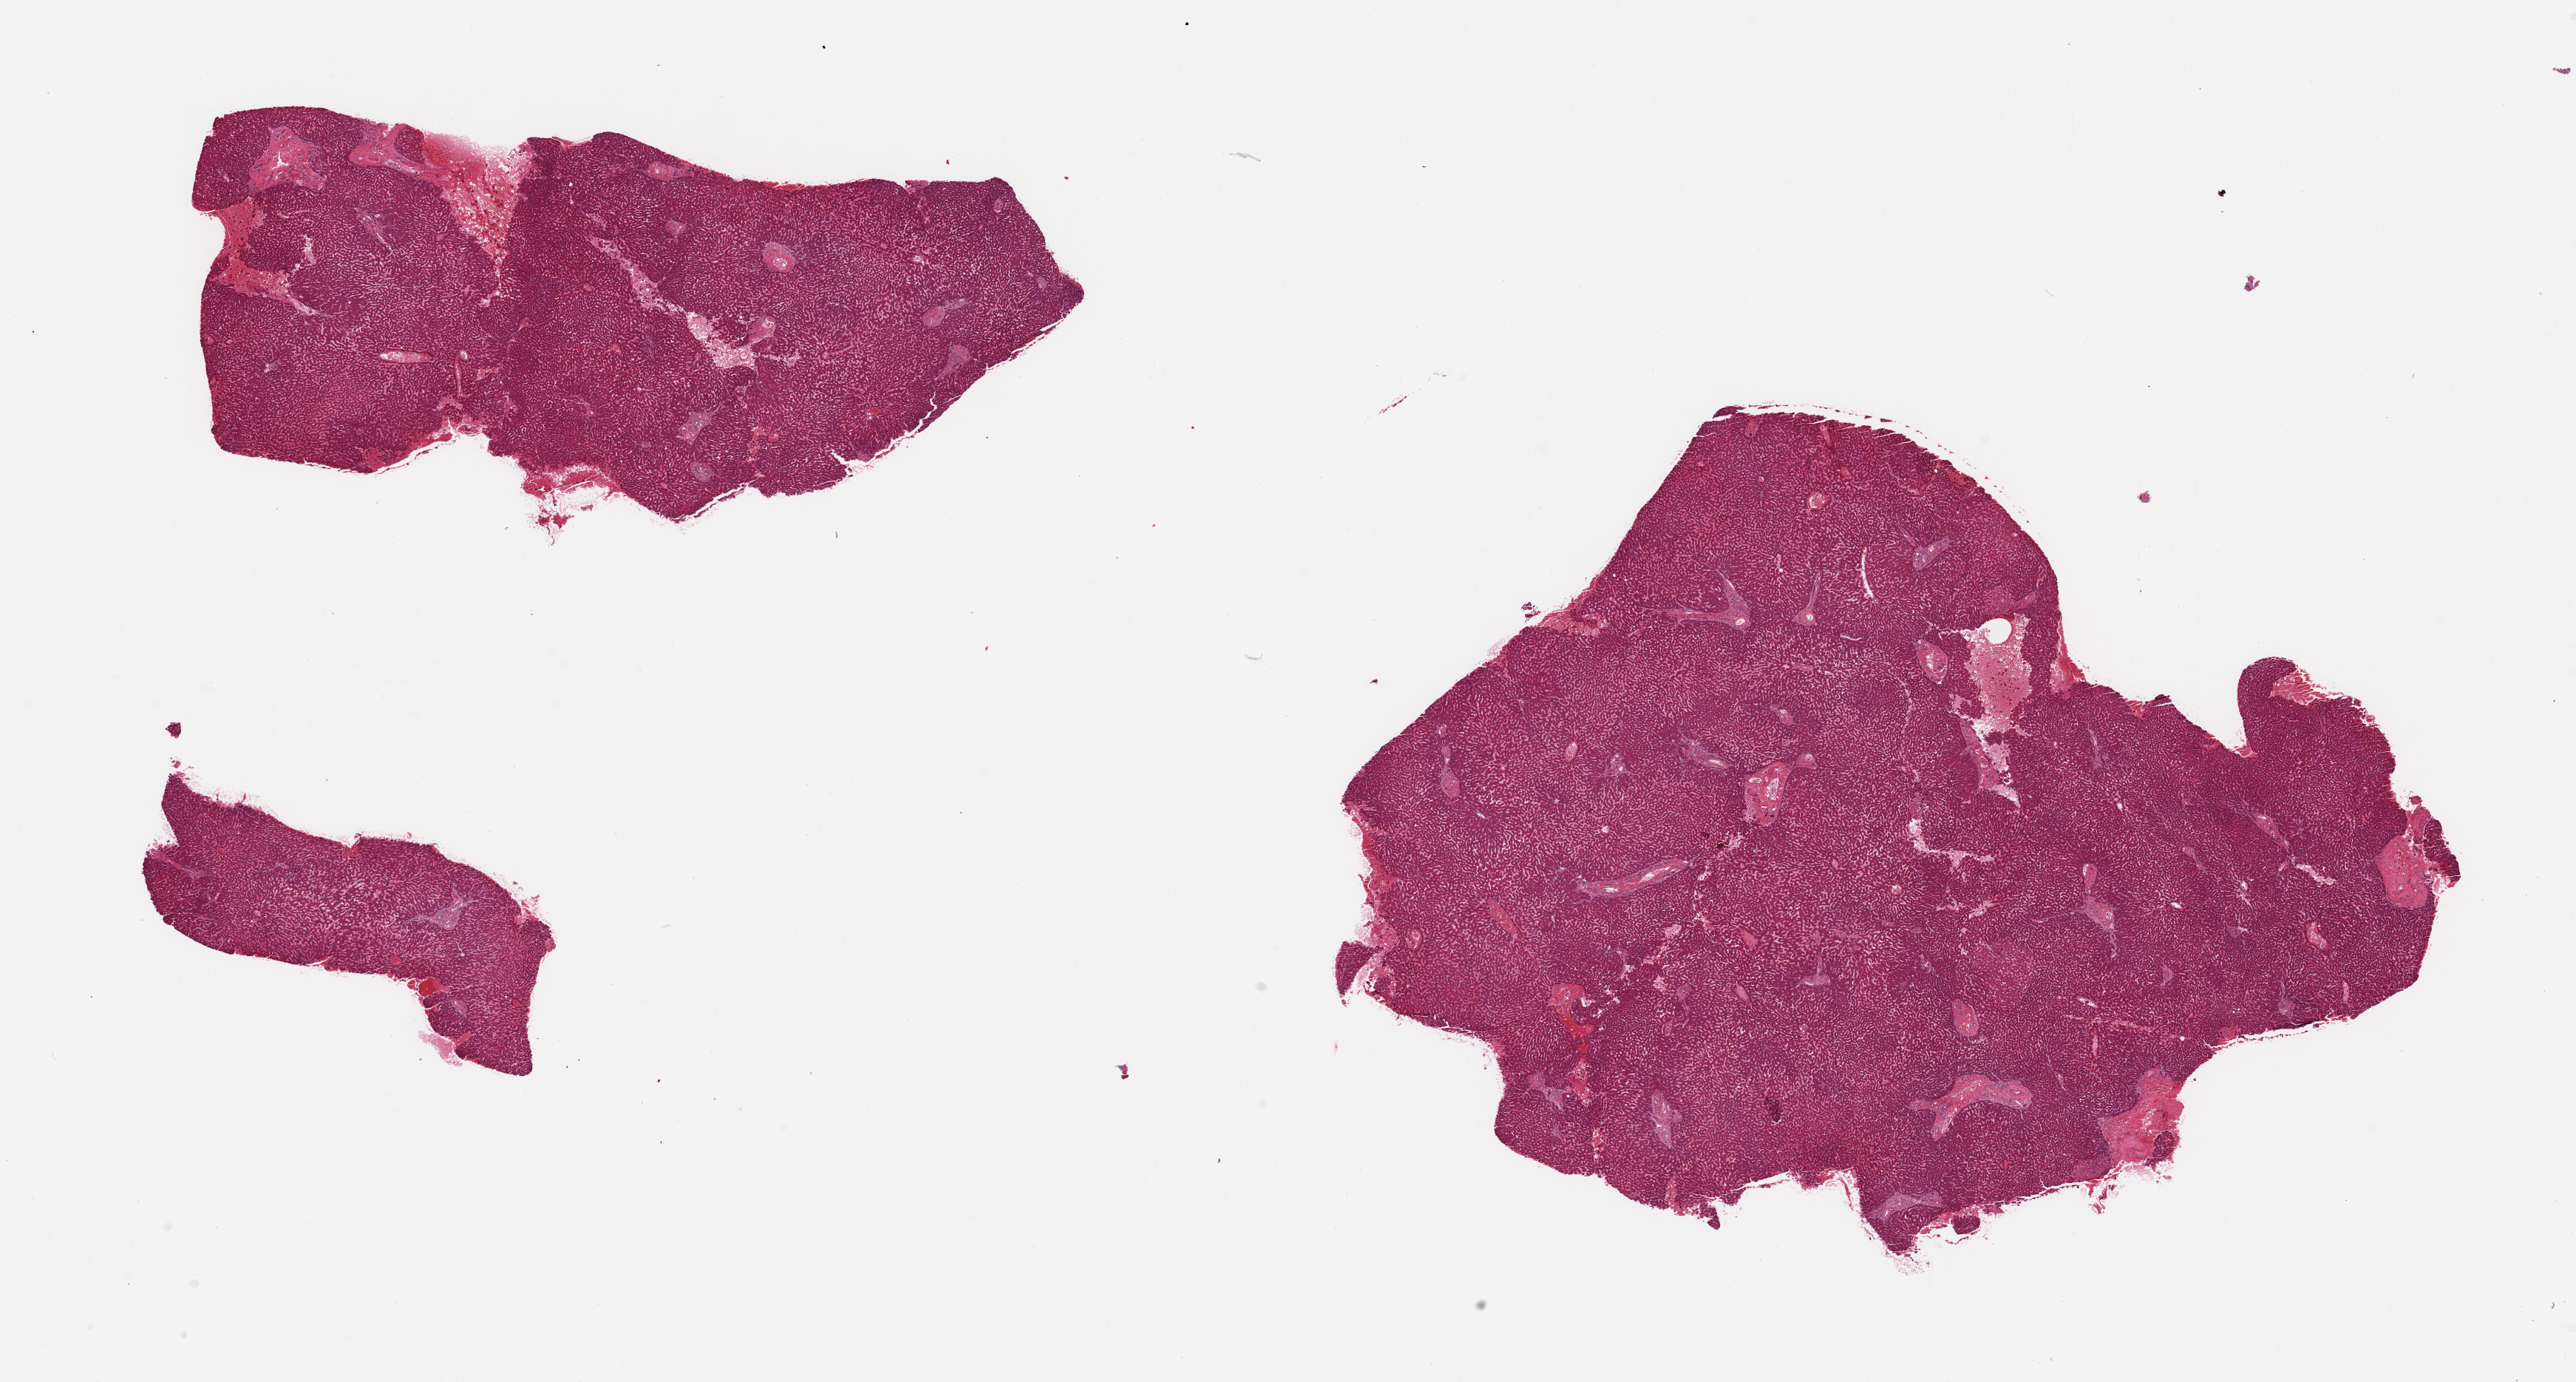
H&E whole-slide image, a low-resolution overview of the entire scanned area, about 27.6 x 14.8 mm (acquisition: 20x scan). PAXgene-fixed paraffin-embedded (PFPE) section. Target tissue: liver. Tissue donor sample.
Pathologist's review note for this sample: 2 pieces, no abnormalities.